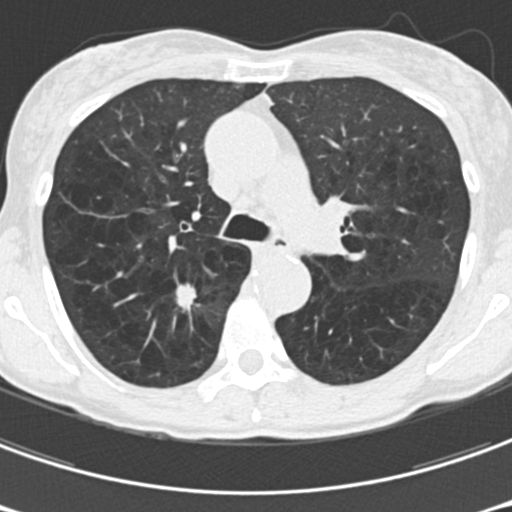
Chest CT (low-dose screening protocol), one axial image. Third annual screen. Lung window (W 1500 / L -600 HU). Female, age 61 years at enrolment. Current smoker at enrolment.
• Lesion marked by an expert reader, box from (x=162, y=271) to (x=222, y=328) px.
• The screening reader recorded 2 non-calcified nodules or masses ≥4 mm on this exam (right upper lobe, right upper lobe); which of them this box marks is not recorded.
• Participant outcome: lung cancer diagnosed 77 days after this screen — non-small cell carcinoma, right upper lobe, undifferentiated (G4), stage IA (AJCC 6th edition), 15 mm at pathology.